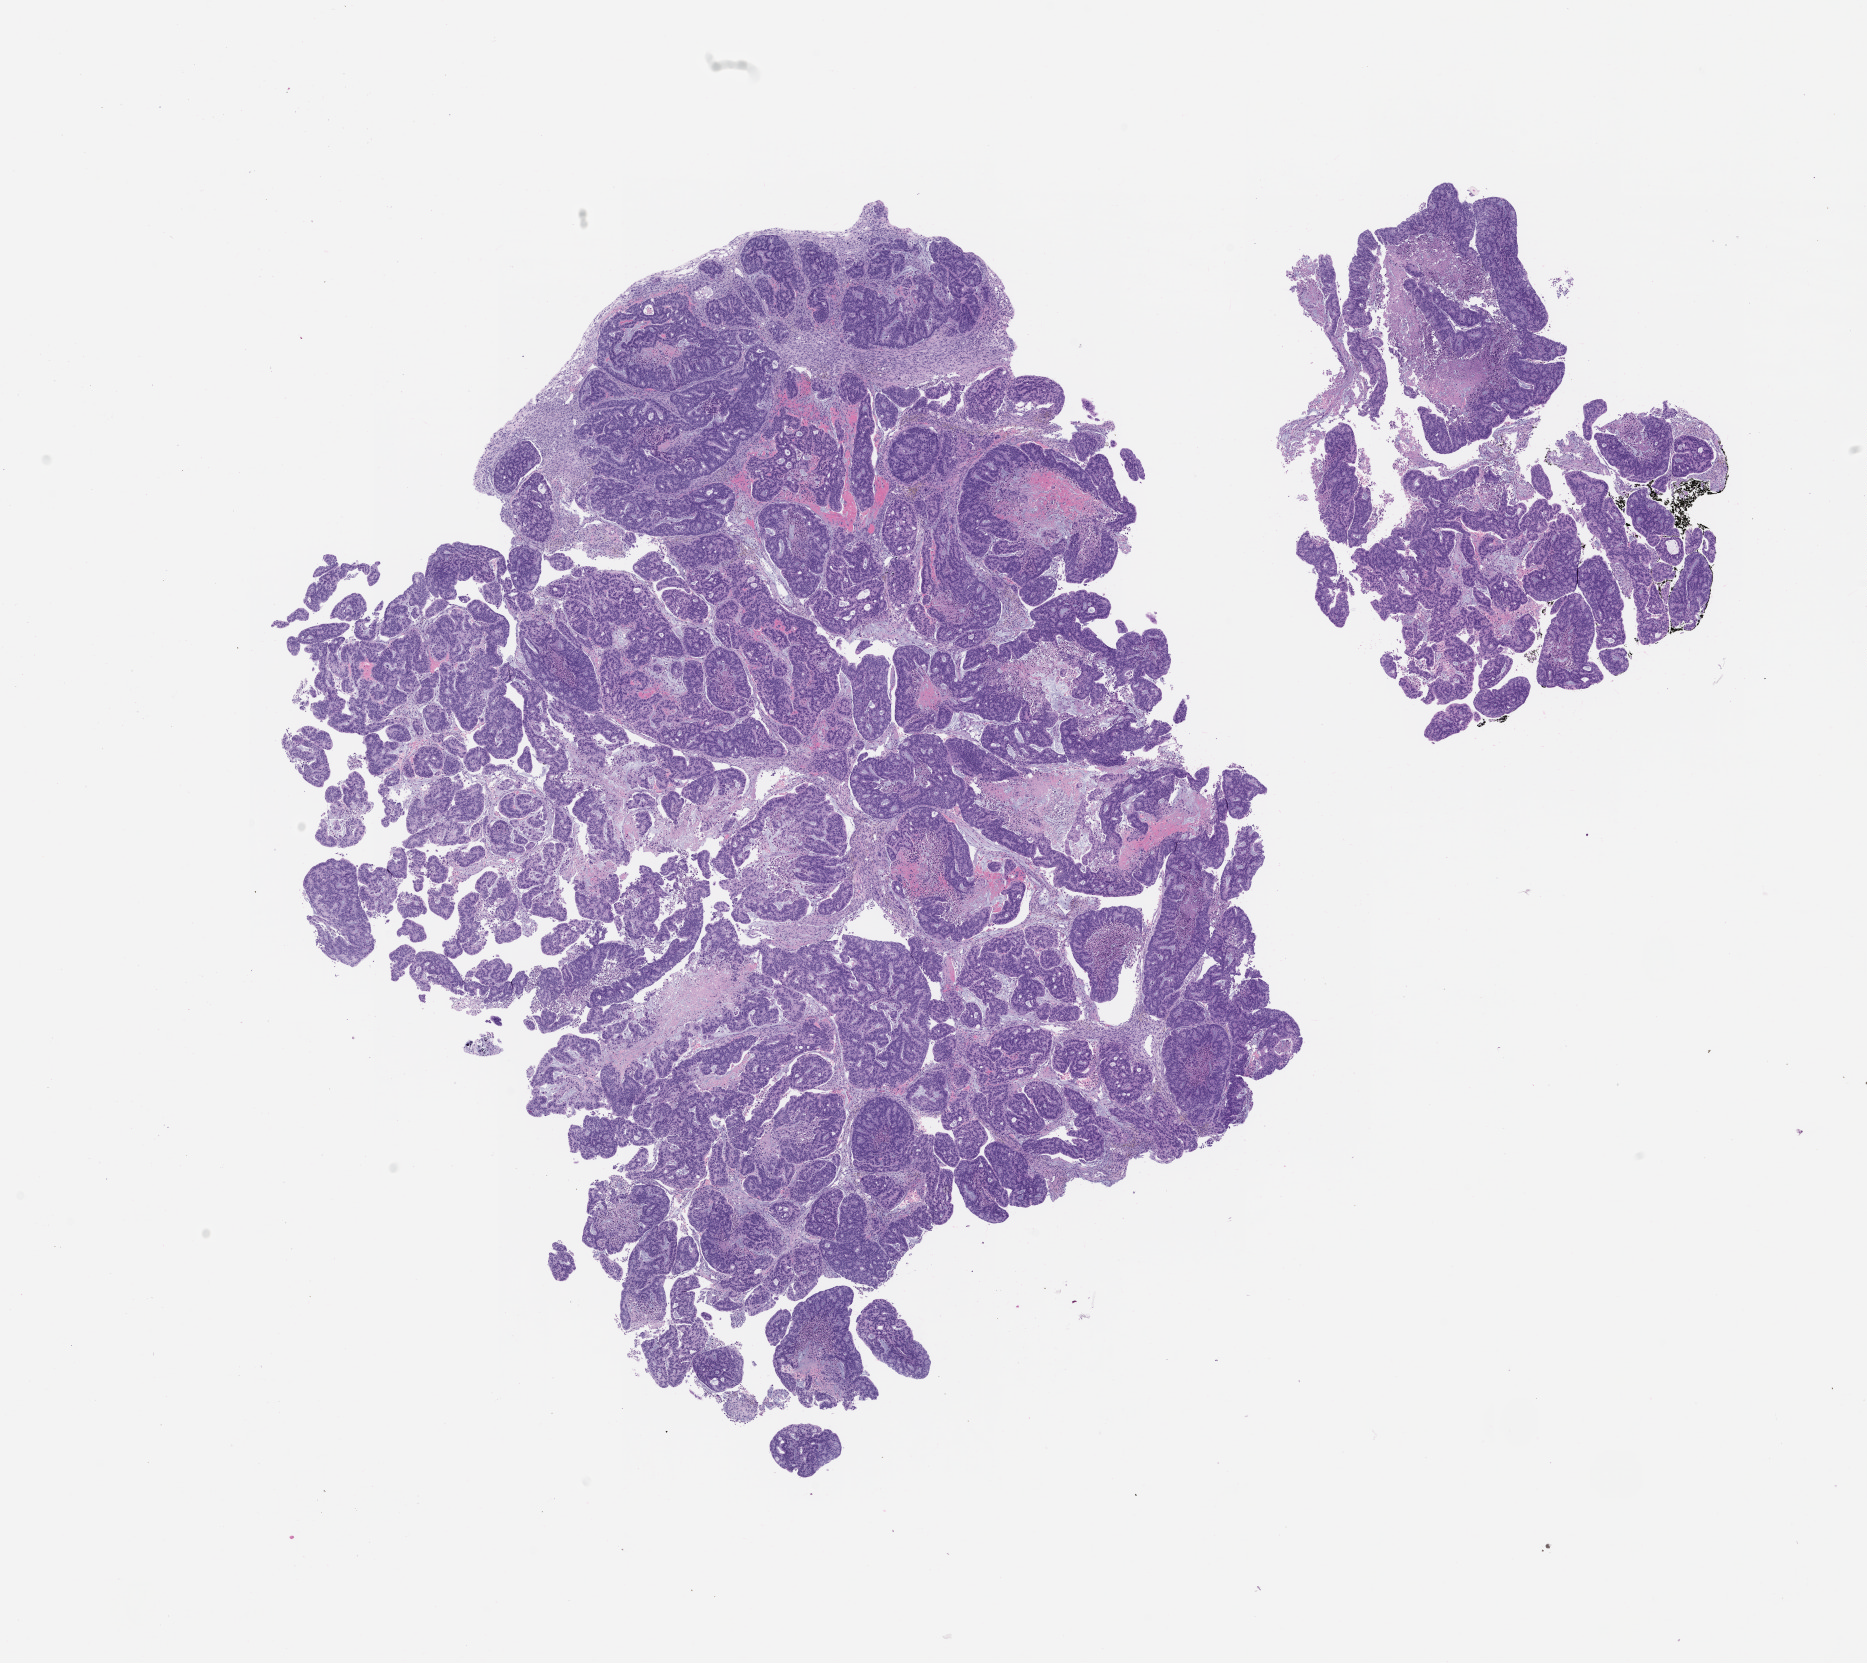
H&E whole-slide image of a patient-derived xenograft (PDX) tumor grown in a mouse, passage 1 — a low-resolution overview of the entire scanned area, about 15.0 x 13.3 mm; formalin-fixed, paraffin-embedded (FFPE) tissue; originating tumor site category: colon.
• originating patient diagnosis: Colon Adenocarcinoma